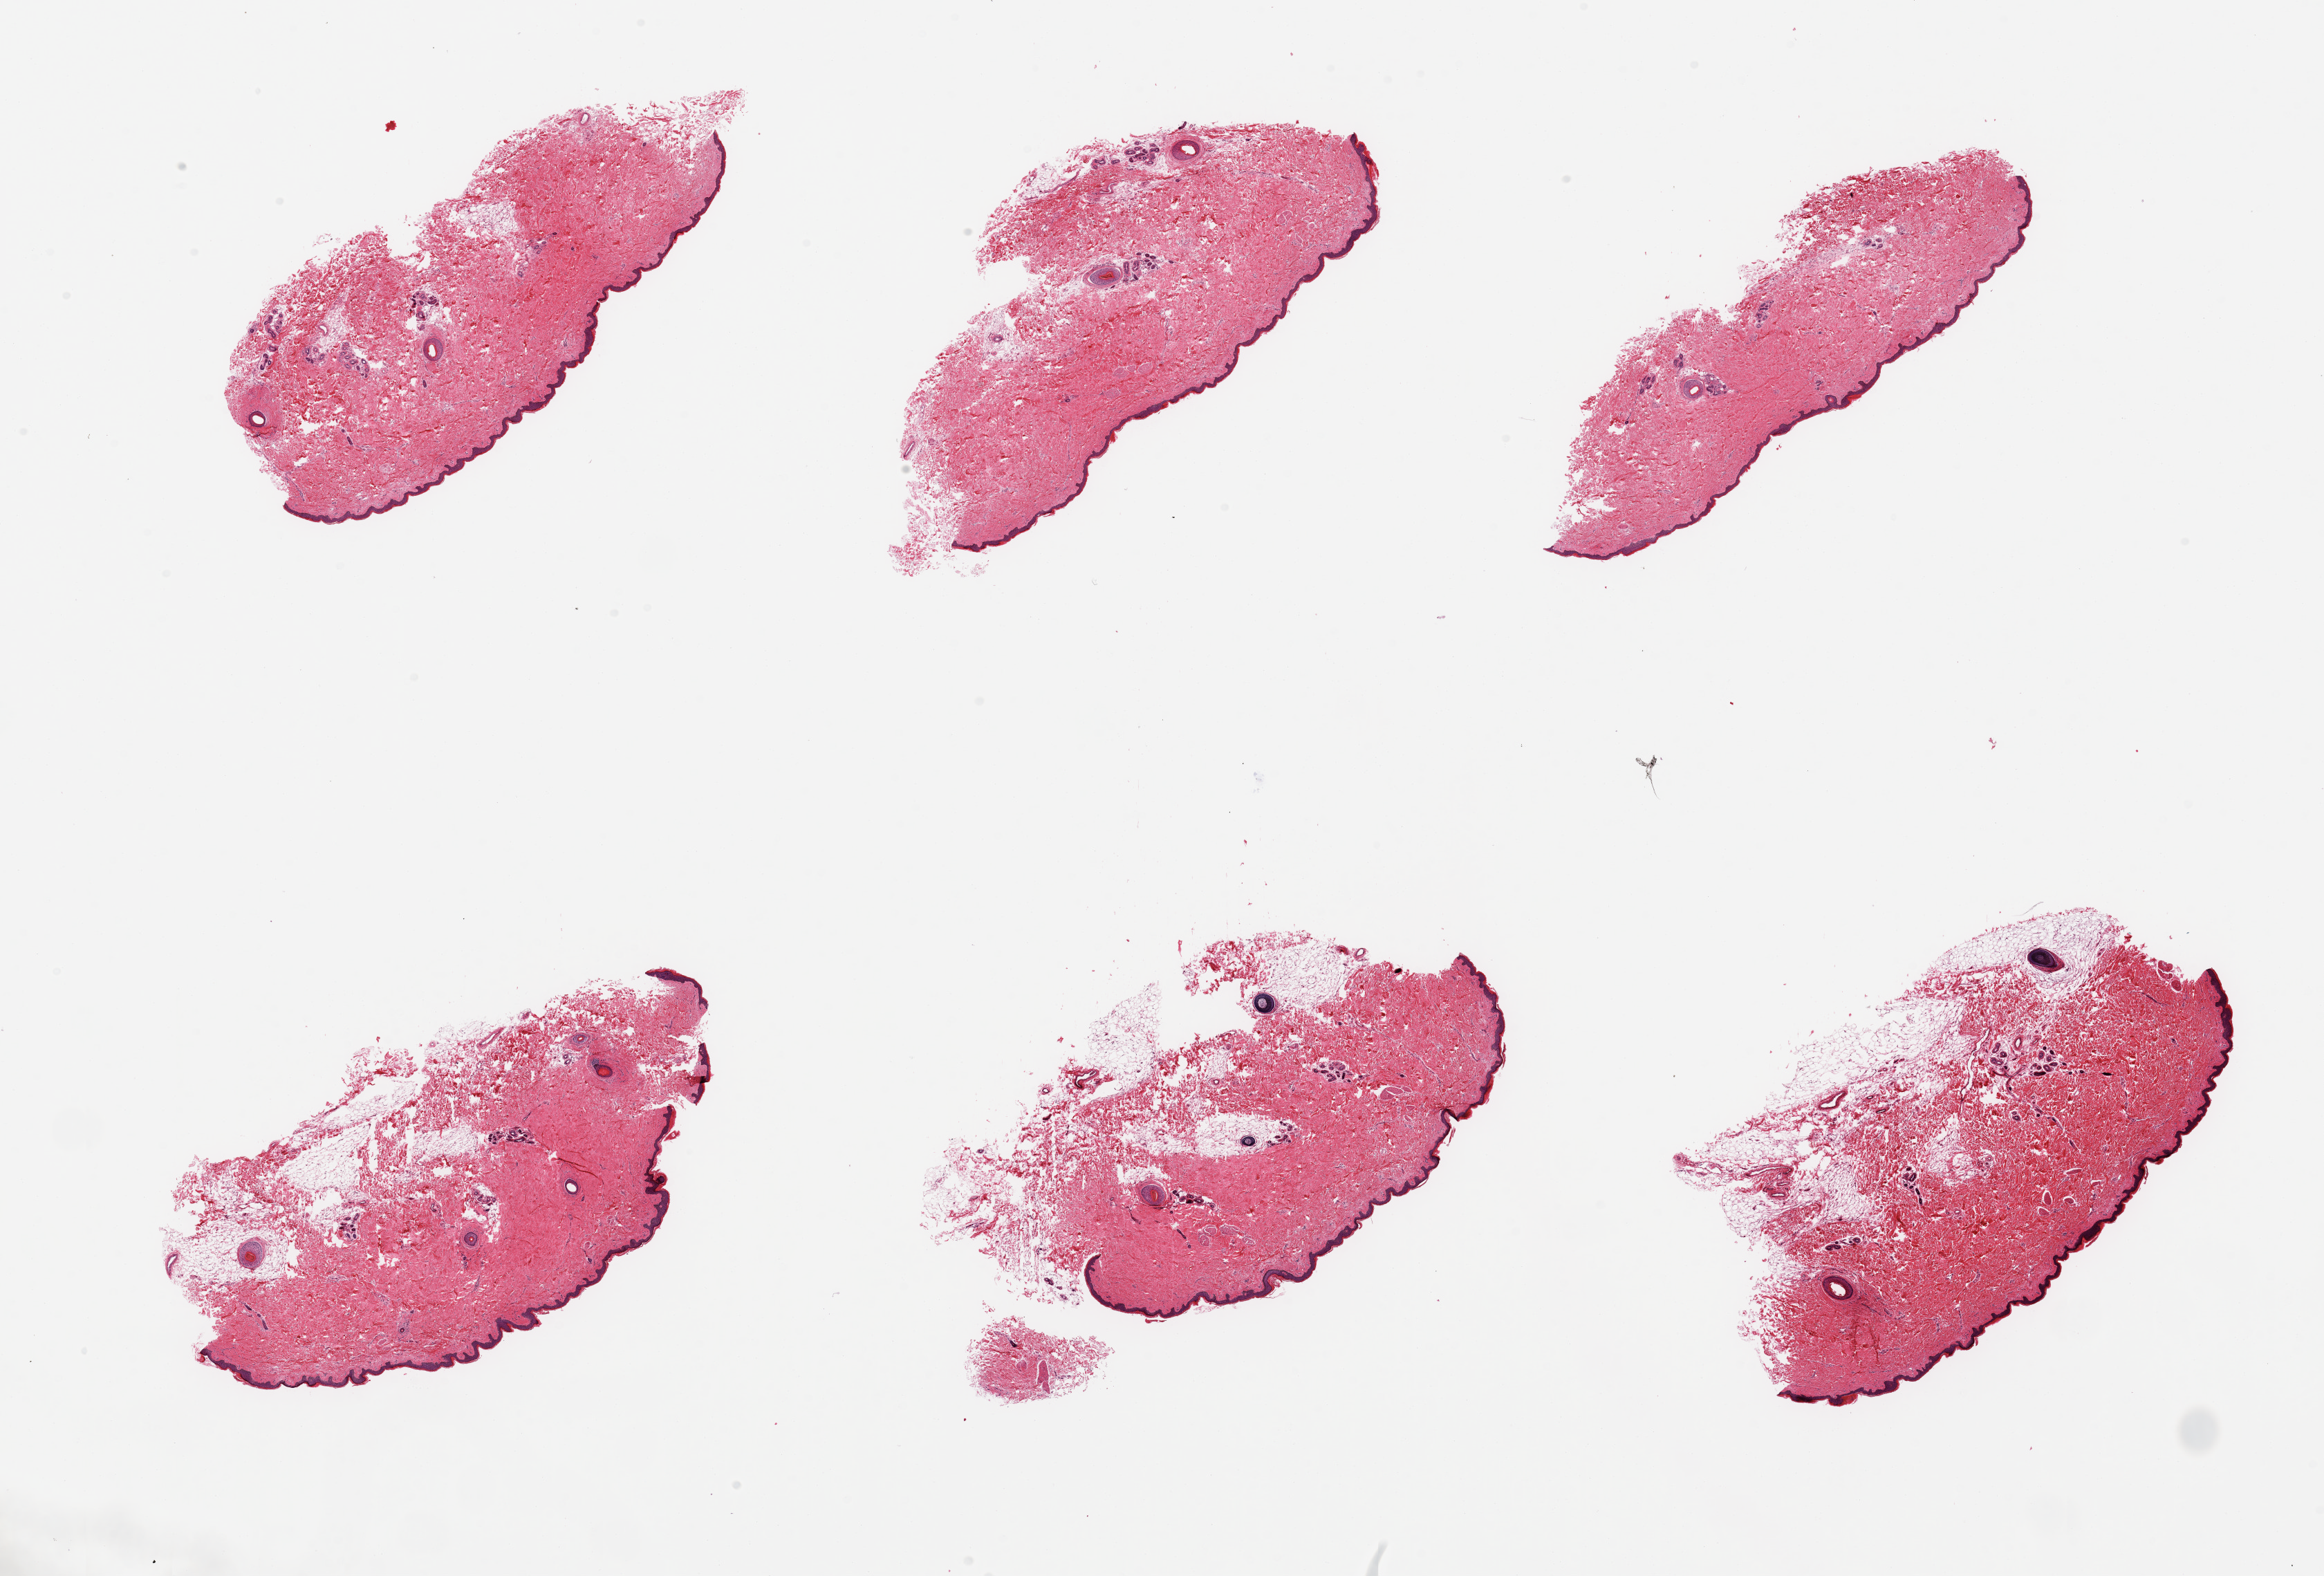
Haematoxylin and eosin whole-slide image, a low-resolution overview of the entire scanned area, about 26.6 x 18.0 mm (slide scanned at 20x); PAXgene-fixed paraffin-embedded (PFPE) section; target tissue: skin of suprapubic region; tissue donor sample. Donor: female.
Review note (as recorded): 6 pieces; 10% dermal fat.